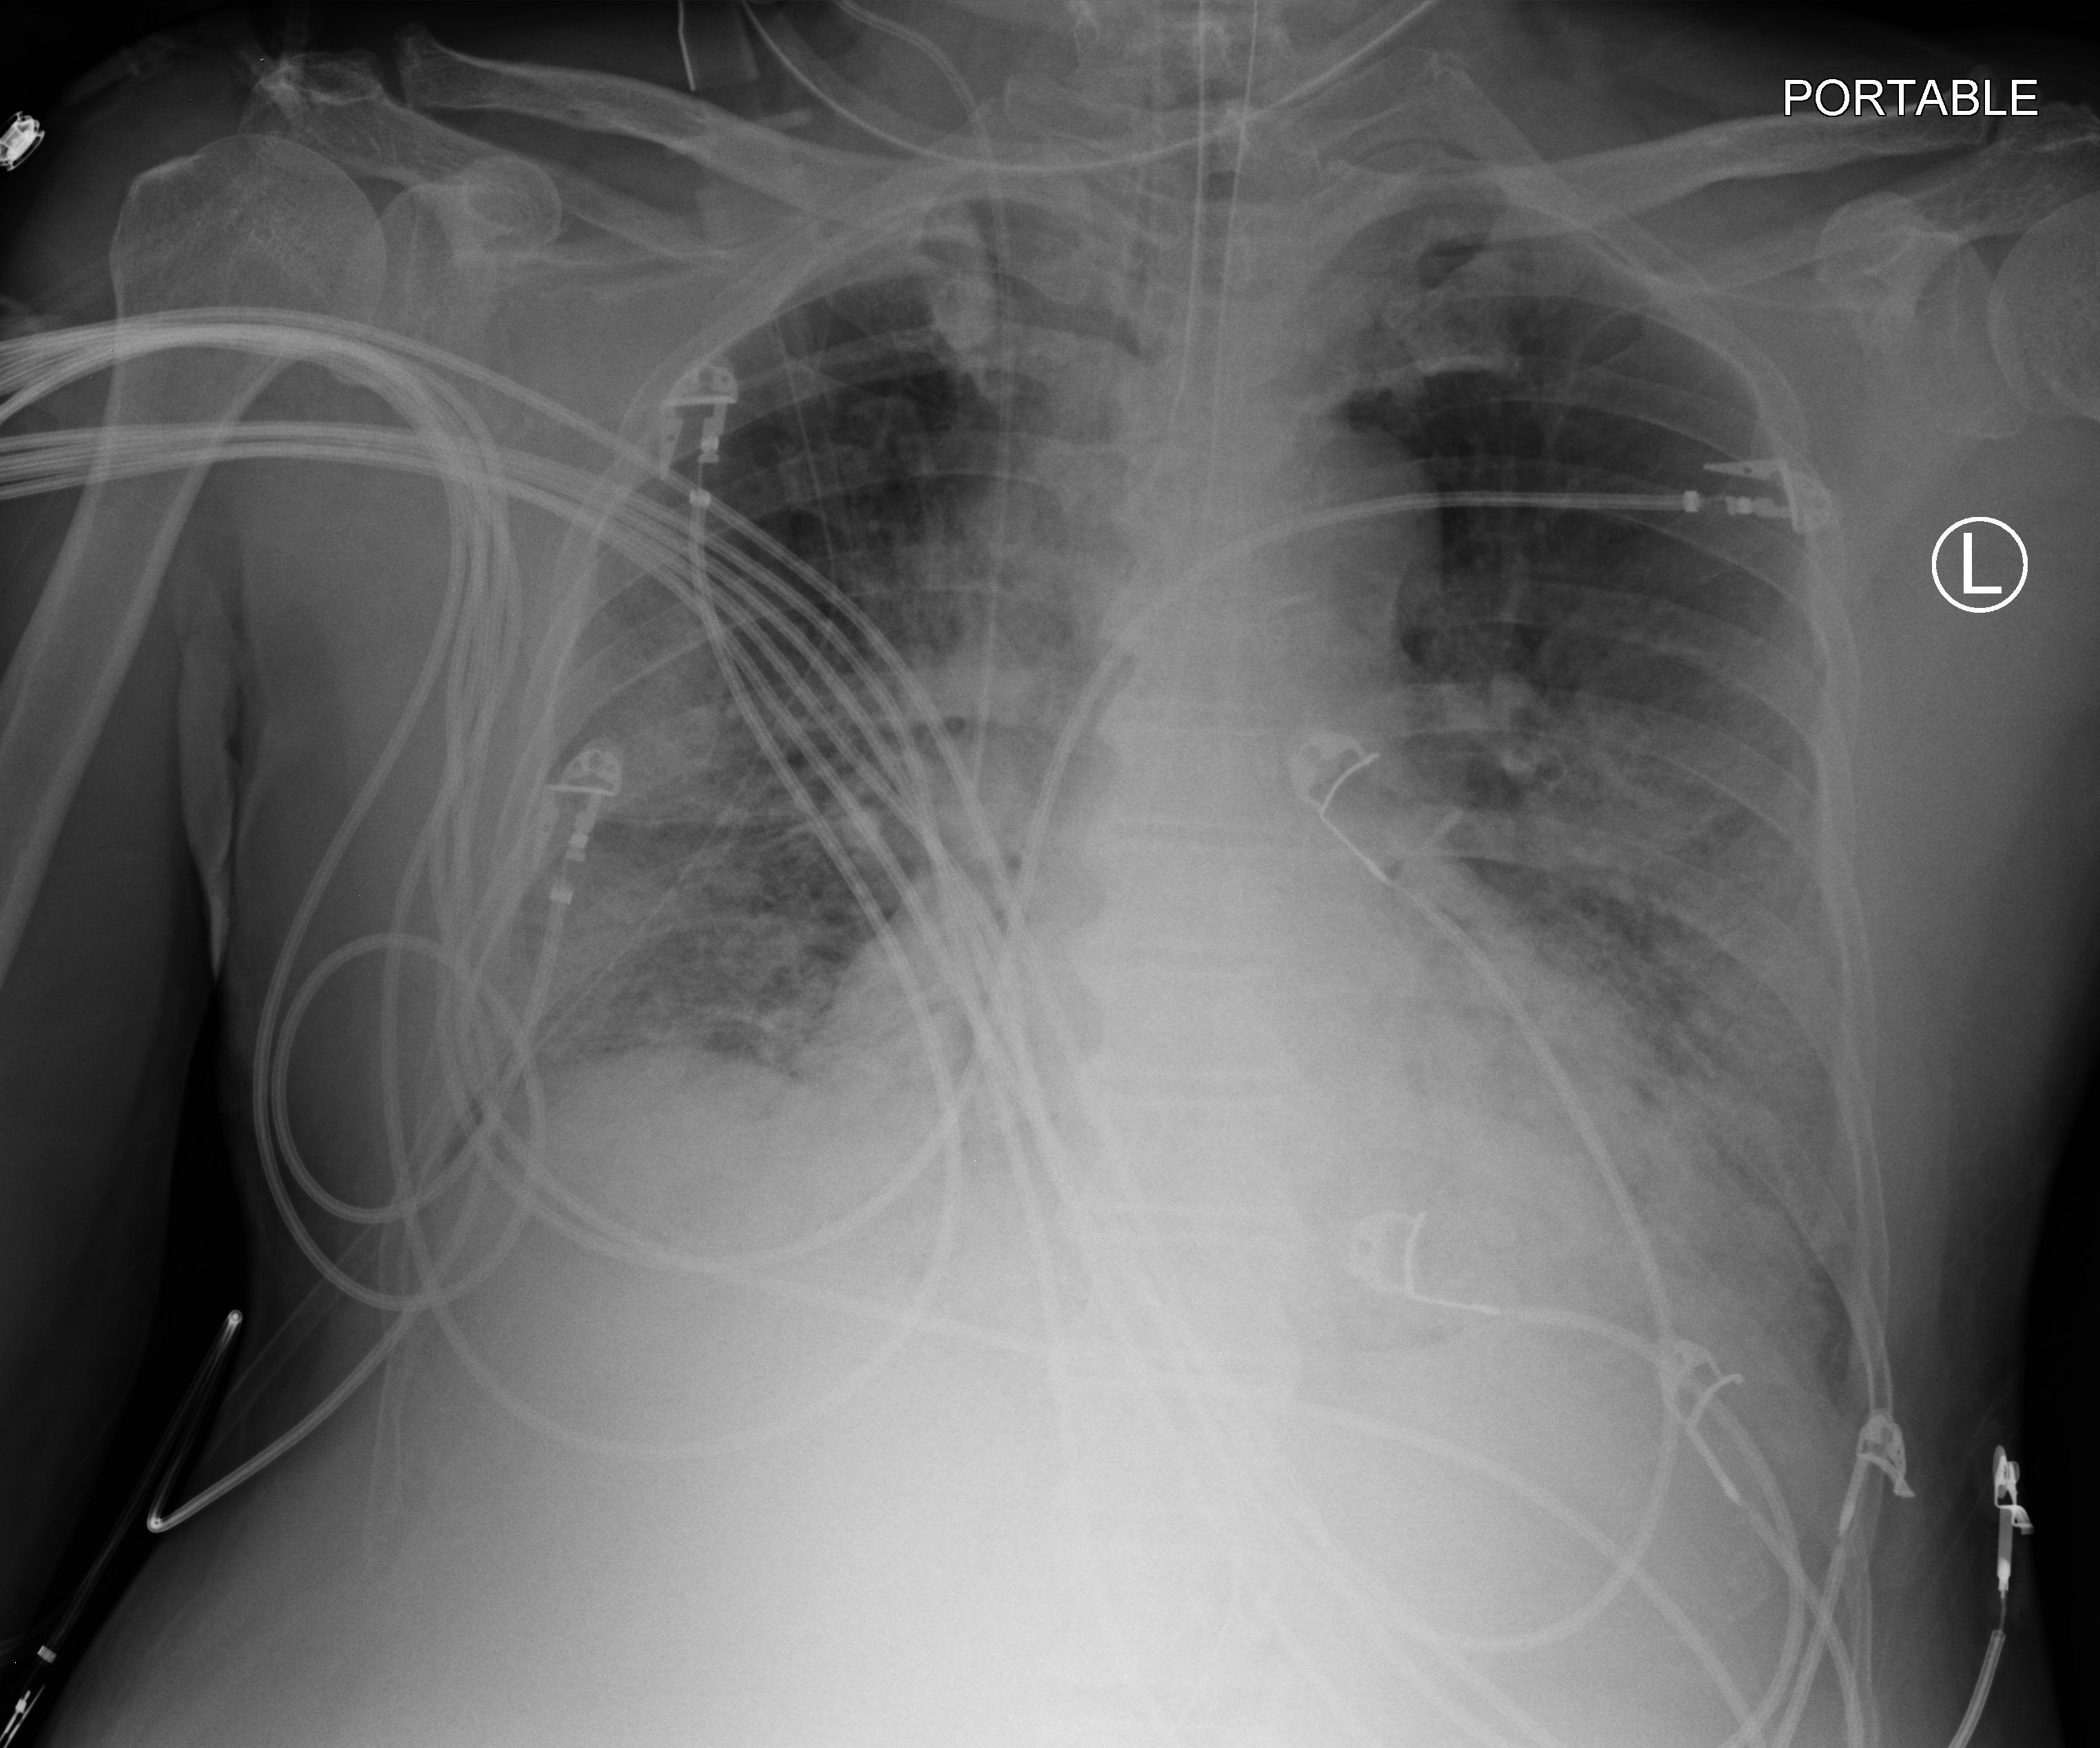
Portable chest radiograph, anteroposterior (AP) projection. Patient hospitalised with COVID-19; male, aged 60–74 years.
Hospital-stay facts (about this admission, not read from this image; timing relative to this image not recorded): mechanically ventilated during this hospital stay: yes.